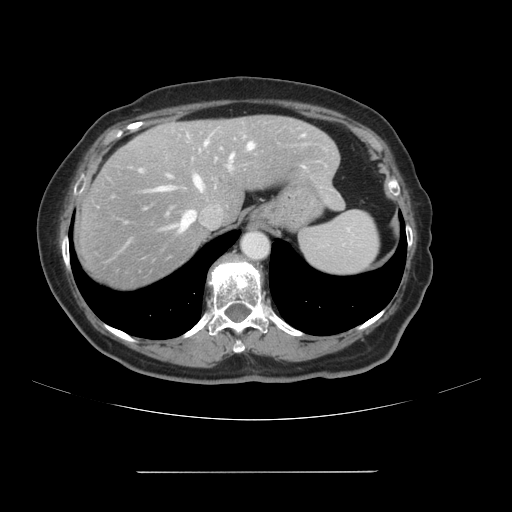
Contrast-enhanced abdominal CT, one axial slice. Slice 83 of 111 in the series (ordered by position). 120 kVp. Soft-tissue window (W 400 / L 40 HU). 2.5 mm slice thickness. 512 × 512 image matrix, field of view 400 × 400 mm. Female patient, age 74 years. From the clinical record (not read from this slice): diagnosis: colorectal cancer liver metastases, imaged before liver resection; multiple liver metastases: yes; largest metastasis: 1.1 cm; disease in both lobes: yes.
Structures marked on this image (manually delineated by an expert):
- hepatic veins: box from (x=154, y=142) to (x=253, y=230) px
- liver: (x=73, y=116)–(x=342, y=292)
- planned liver remnant (the part of the liver to remain after resection): (x=163, y=116)–(x=343, y=220)
- portal vein (with intrahepatic branches): (x=141, y=162)–(x=232, y=171)